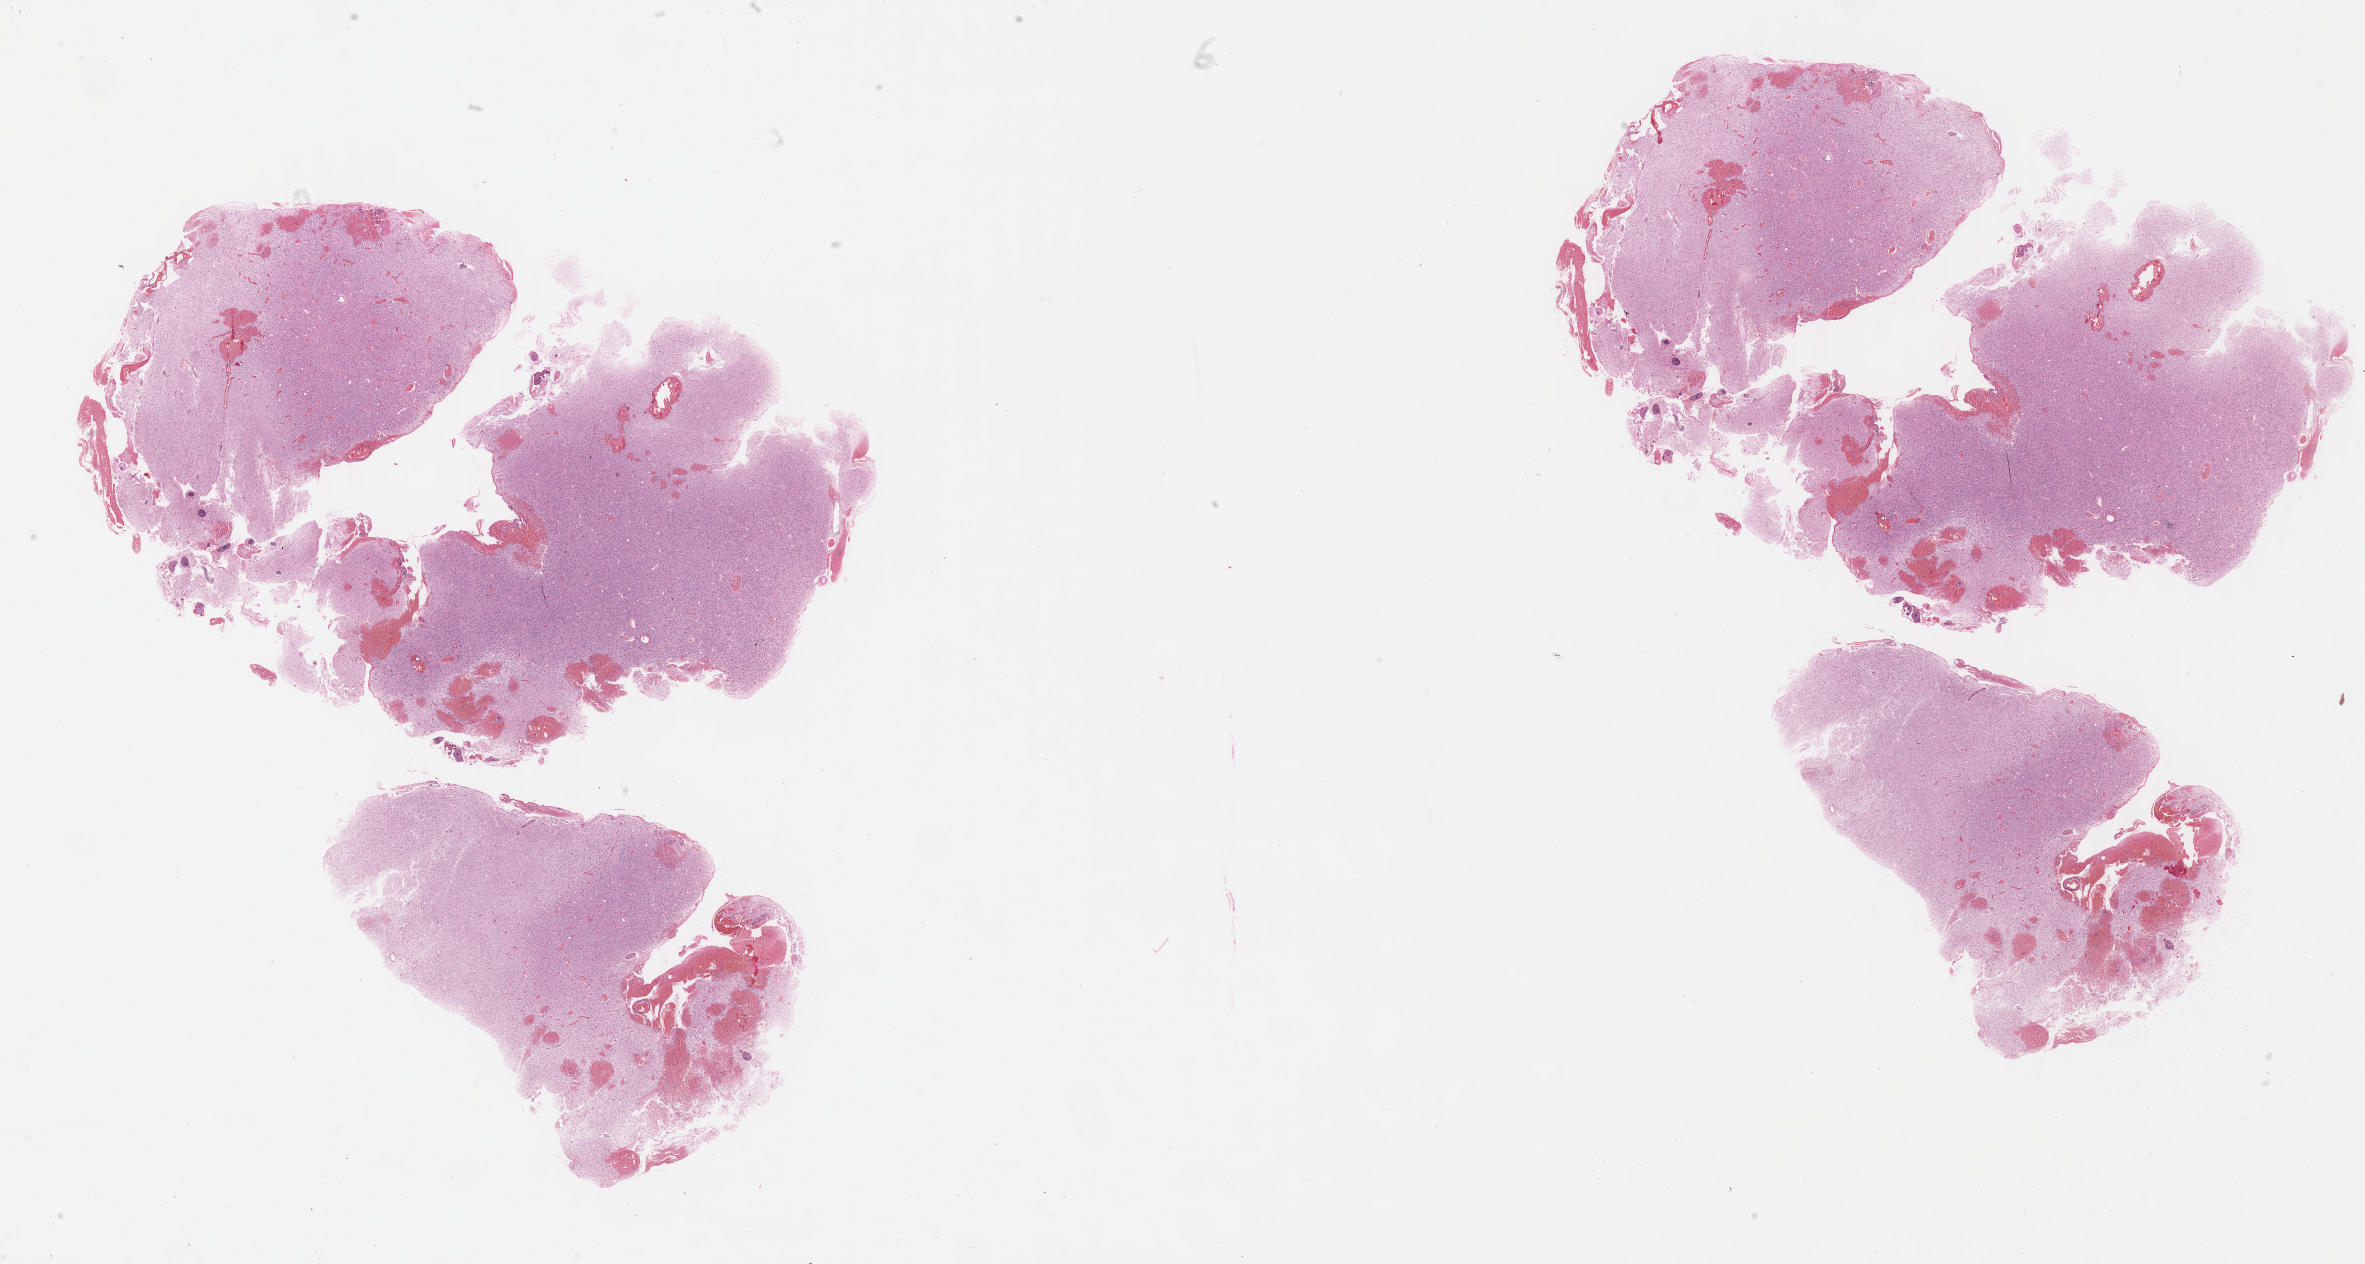
Whole-slide histology image, H&E, whole scanned area (about 38.2 x 20.4 mm) shown as a low-resolution overview. FFPE section. Primary tumour sample from the brain. Male, age 36 years at initial diagnosis. Histologic grade: G2 (moderately differentiated).
Laterality: left. Pathologic diagnosis: Mixed glioma.